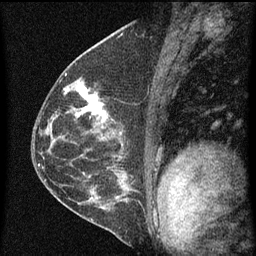
Breast MRI (dynamic contrast-enhanced), one sagittal slice. Slice 34 of 60 in the series (ordered by position). Dynamic contrast-enhanced series, image 2 of 4 at this slice position (ordered by acquisition). 1.5 T. TE 4.2 ms, TR 8 ms. 2 mm slice thickness. 256 × 256 image matrix, field of view 180 × 180 mm. Female patient, age 48 years.
Structures marked on this image (semi-automatic segmentation, software-assisted and operator-edited):
- analysis volume of interest (the breast-tissue region the enhancement analysis was run in; not a lesion): bounding box <73,82,115,139> (left, top, right, bottom; pixels)
- tumour enhancement mask (voxels above the 70 % enhancement threshold inside the analysis volume of interest): <76,86,113,129>